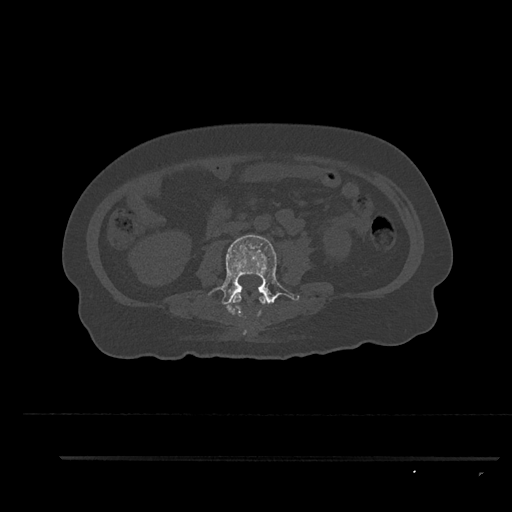
CT including the spine, one axial slice; slice 102 of 797 in the series (ordered by position); reconstruction kernel Br40s/3; 120 kVp; bone window (W 1800 / L 400 HU); 0.5 mm slice thickness; 512 × 512 image matrix, field of view 408 × 408 mm. Female patient, age 44 years. Case-level facts recorded for this patient, not image findings: primary cancer: renal.
Annotated regions visible in this slice (semi-automatic segmentation, software-assisted and operator-edited):
- L2 vertebra: bounding box [x1, y1, x2, y2] px = [231, 293, 266, 319]
- L3 vertebra: [207, 235, 300, 315]